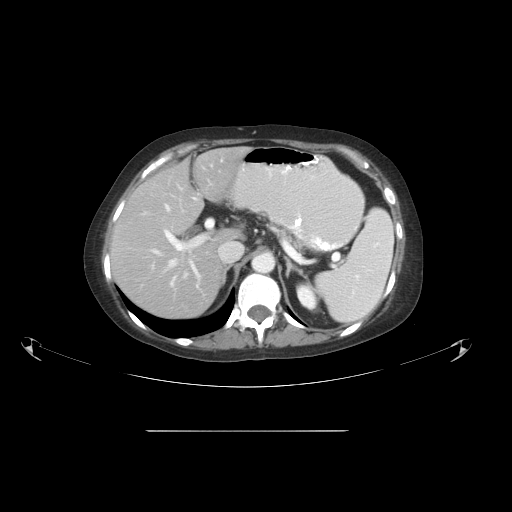
Contrast-enhanced abdominal CT, one axial slice. Slice 35 of 51 in the series (ordered by position). 120 kVp. Intravenous contrast given. Soft-tissue window (W 400 / L 40 HU). 512 × 512 image matrix. Female patient, age 48 years. From the clinical record (not read from this slice): diagnosis: colorectal cancer liver metastases, imaged before liver resection; multiple liver metastases: yes; largest metastasis: 1 cm; chemotherapy before resection: no.
Structures marked on this image (manually delineated by an expert):
- hepatic veins: bounding box [x1, y1, x2, y2] px = [145, 205, 243, 280]
- liver: [111, 148, 249, 320]
- planned liver remnant (the part of the liver to remain after resection): [111, 162, 232, 320]
- portal vein (with intrahepatic branches): [164, 197, 213, 288]
- liver metastasis: [202, 160, 208, 168]